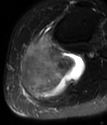
MRI of an extremity soft-tissue mass, one axial slice; T2-weighted fat-saturated; MR volume resampled by the dataset authors to the PET/CT grid (not the native acquisition matrix); 3.27 mm slice thickness; 107 × 125 image matrix, field of view 104 × 122 mm. Female patient. From the clinical record (not read from this slice): histological type: extraskeletal high grade osteogenic sarcoma; grade: high; site of the primary tumour: left calf.
Structures marked on this image (expert contour drawn on MRI and transferred to this co-registered scan by the dataset authors):
- gross tumour volume (mass): bounding box (x1, y1, x2, y2) in pixels: (21, 36, 86, 99)